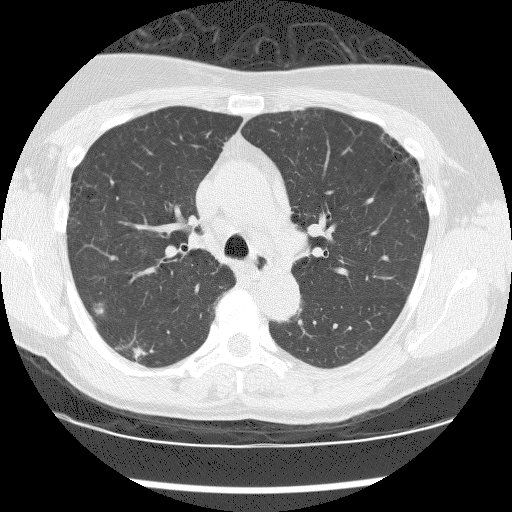
Low-dose screening chest CT, one axial slice; slice 124 of 176 in the series (ordered by position); reconstruction kernel BONE; 120 kVp; lung window (W 1500 / L -600 HU); 2.5 mm slice thickness; 512 × 512 image matrix, field of view 320 × 320 mm.
Annotated regions visible in this slice (outlined manually by an expert reader):
- lesion 1 (tumor, lower lobe of right lung): bounding box (x1, y1, x2, y2) in pixels: (132, 347, 147, 359)